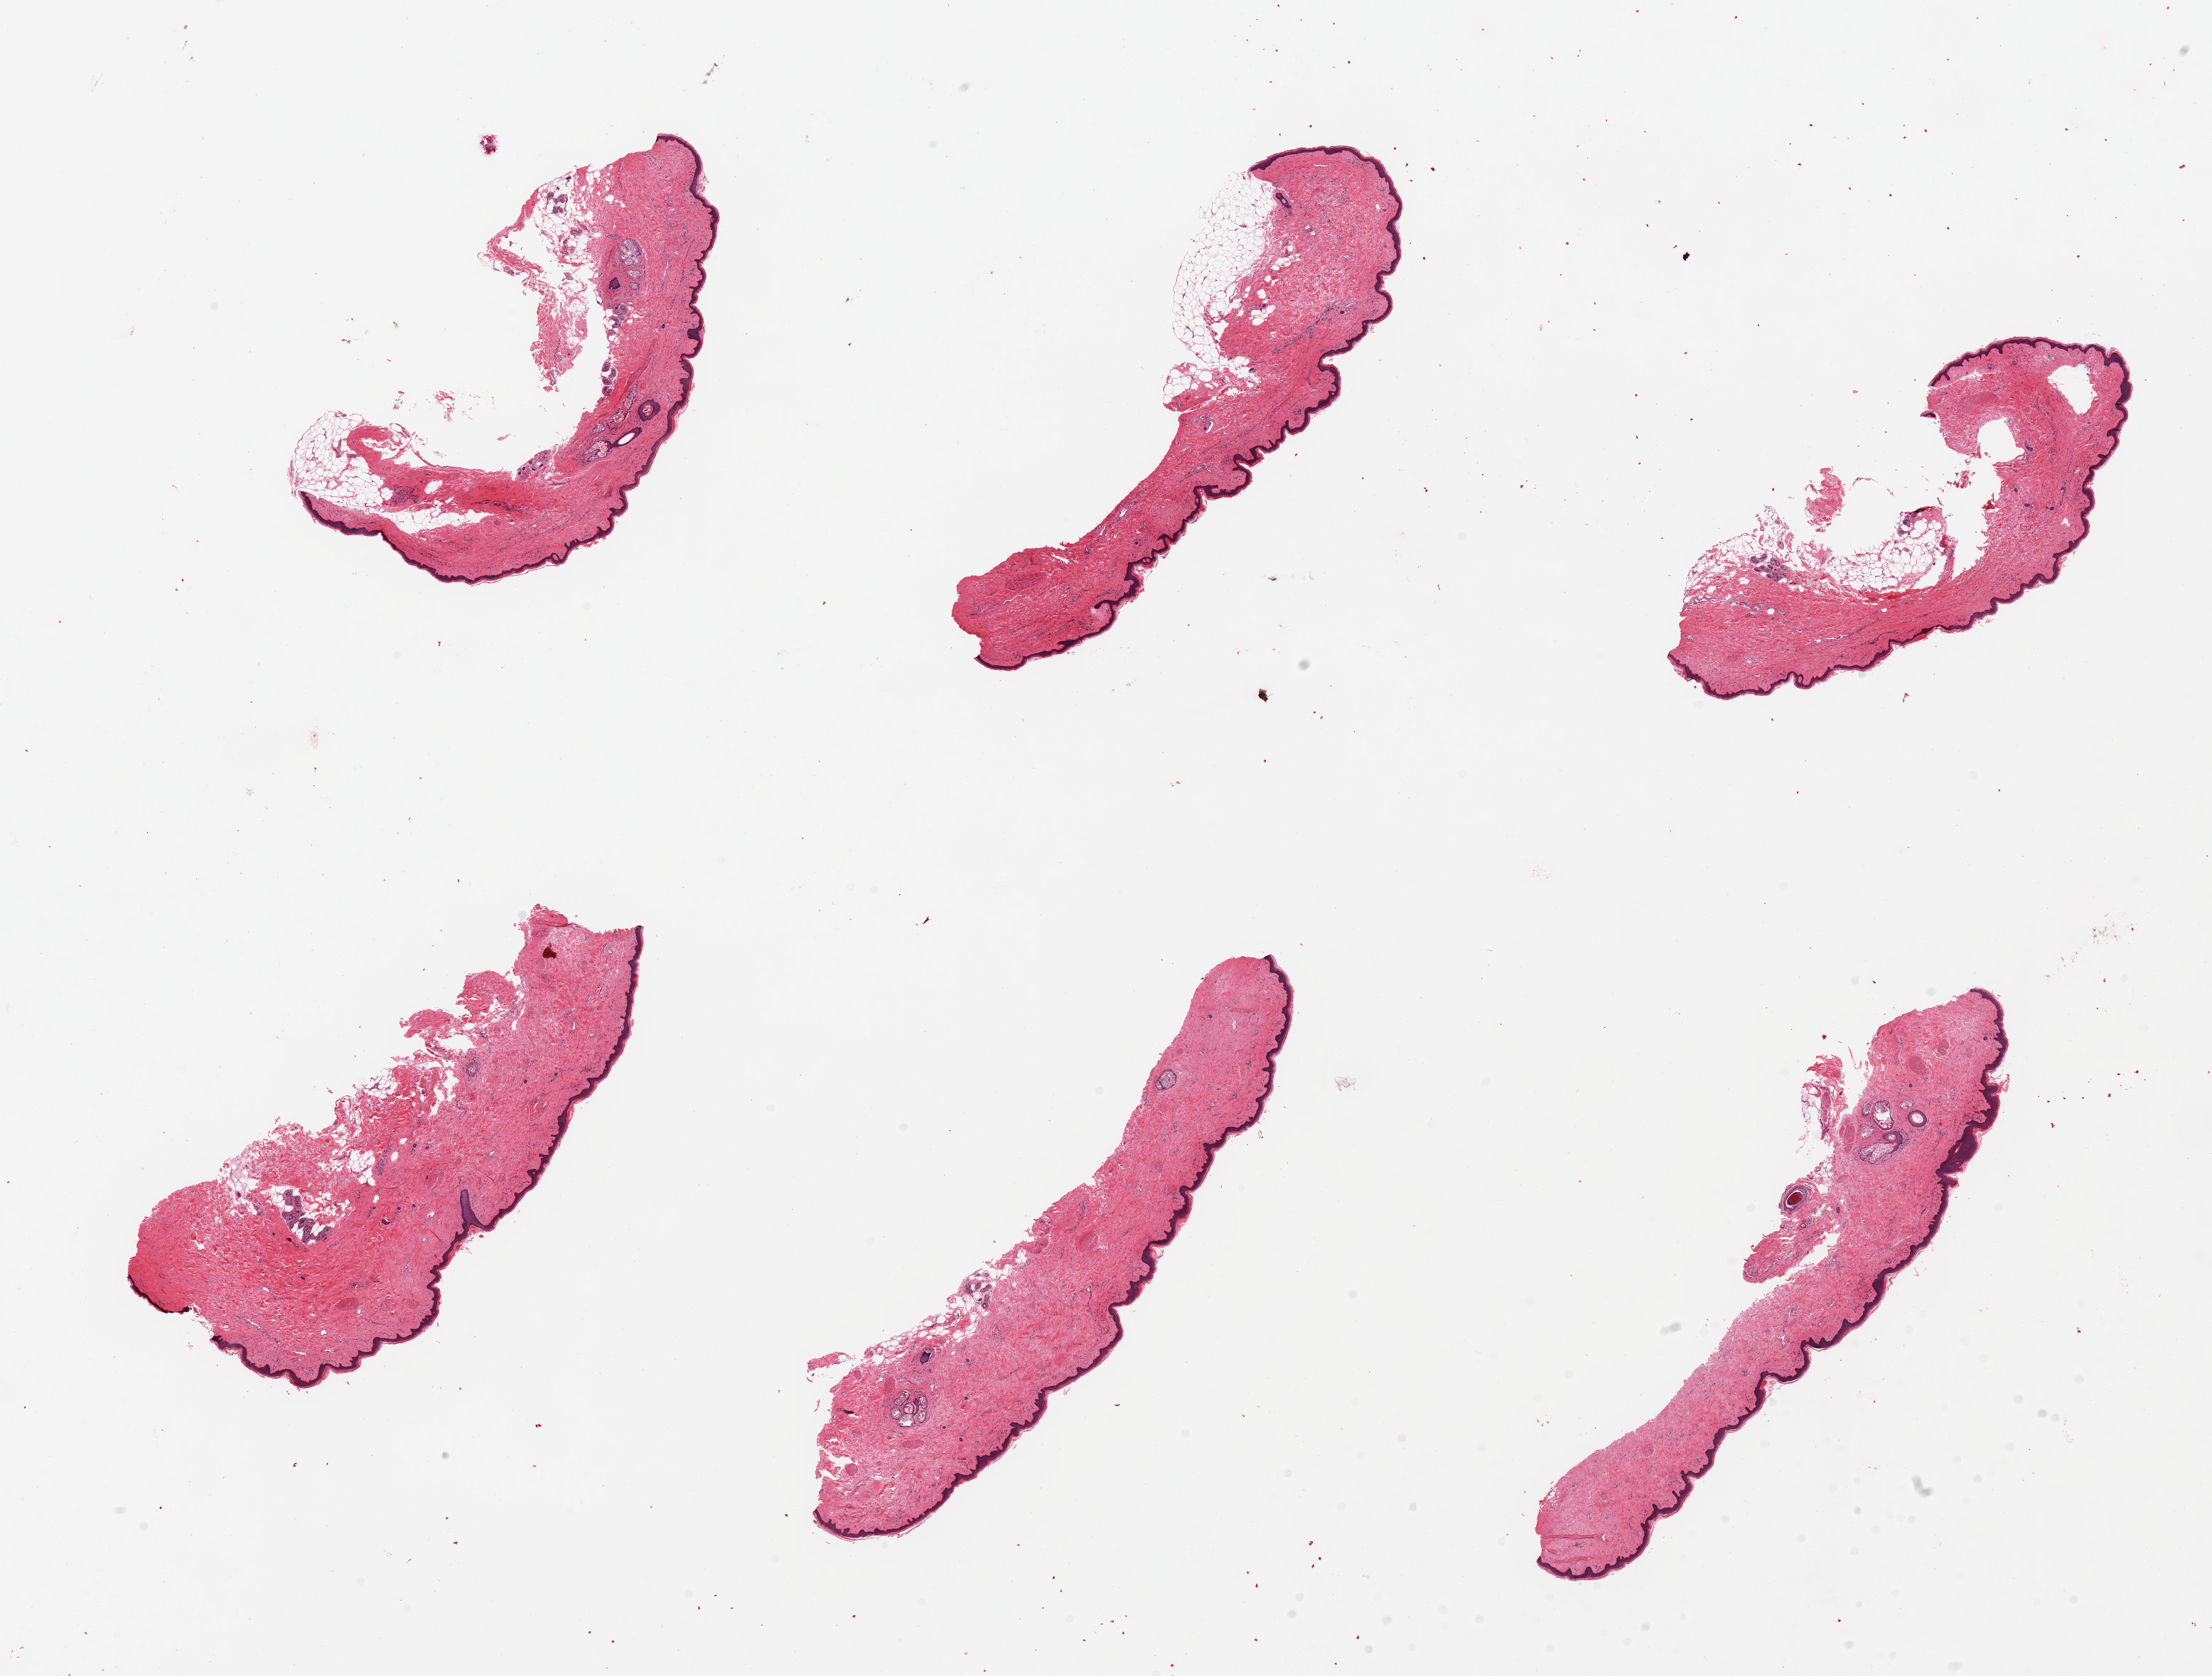
Whole-slide image, H&E stain, shown as a low-resolution overview of the whole scanned area (about 24.6 x 18.6 mm, slide scanned at 20x); PAXgene-fixed paraffin-embedded (PFPE) section; target tissue: skin of suprapubic region; donor tissue sample. Donor sex: female.
• review note (as recorded): 6 pieces: 1 with 10% subcutaneous fat; otherwise minimal dermal fat